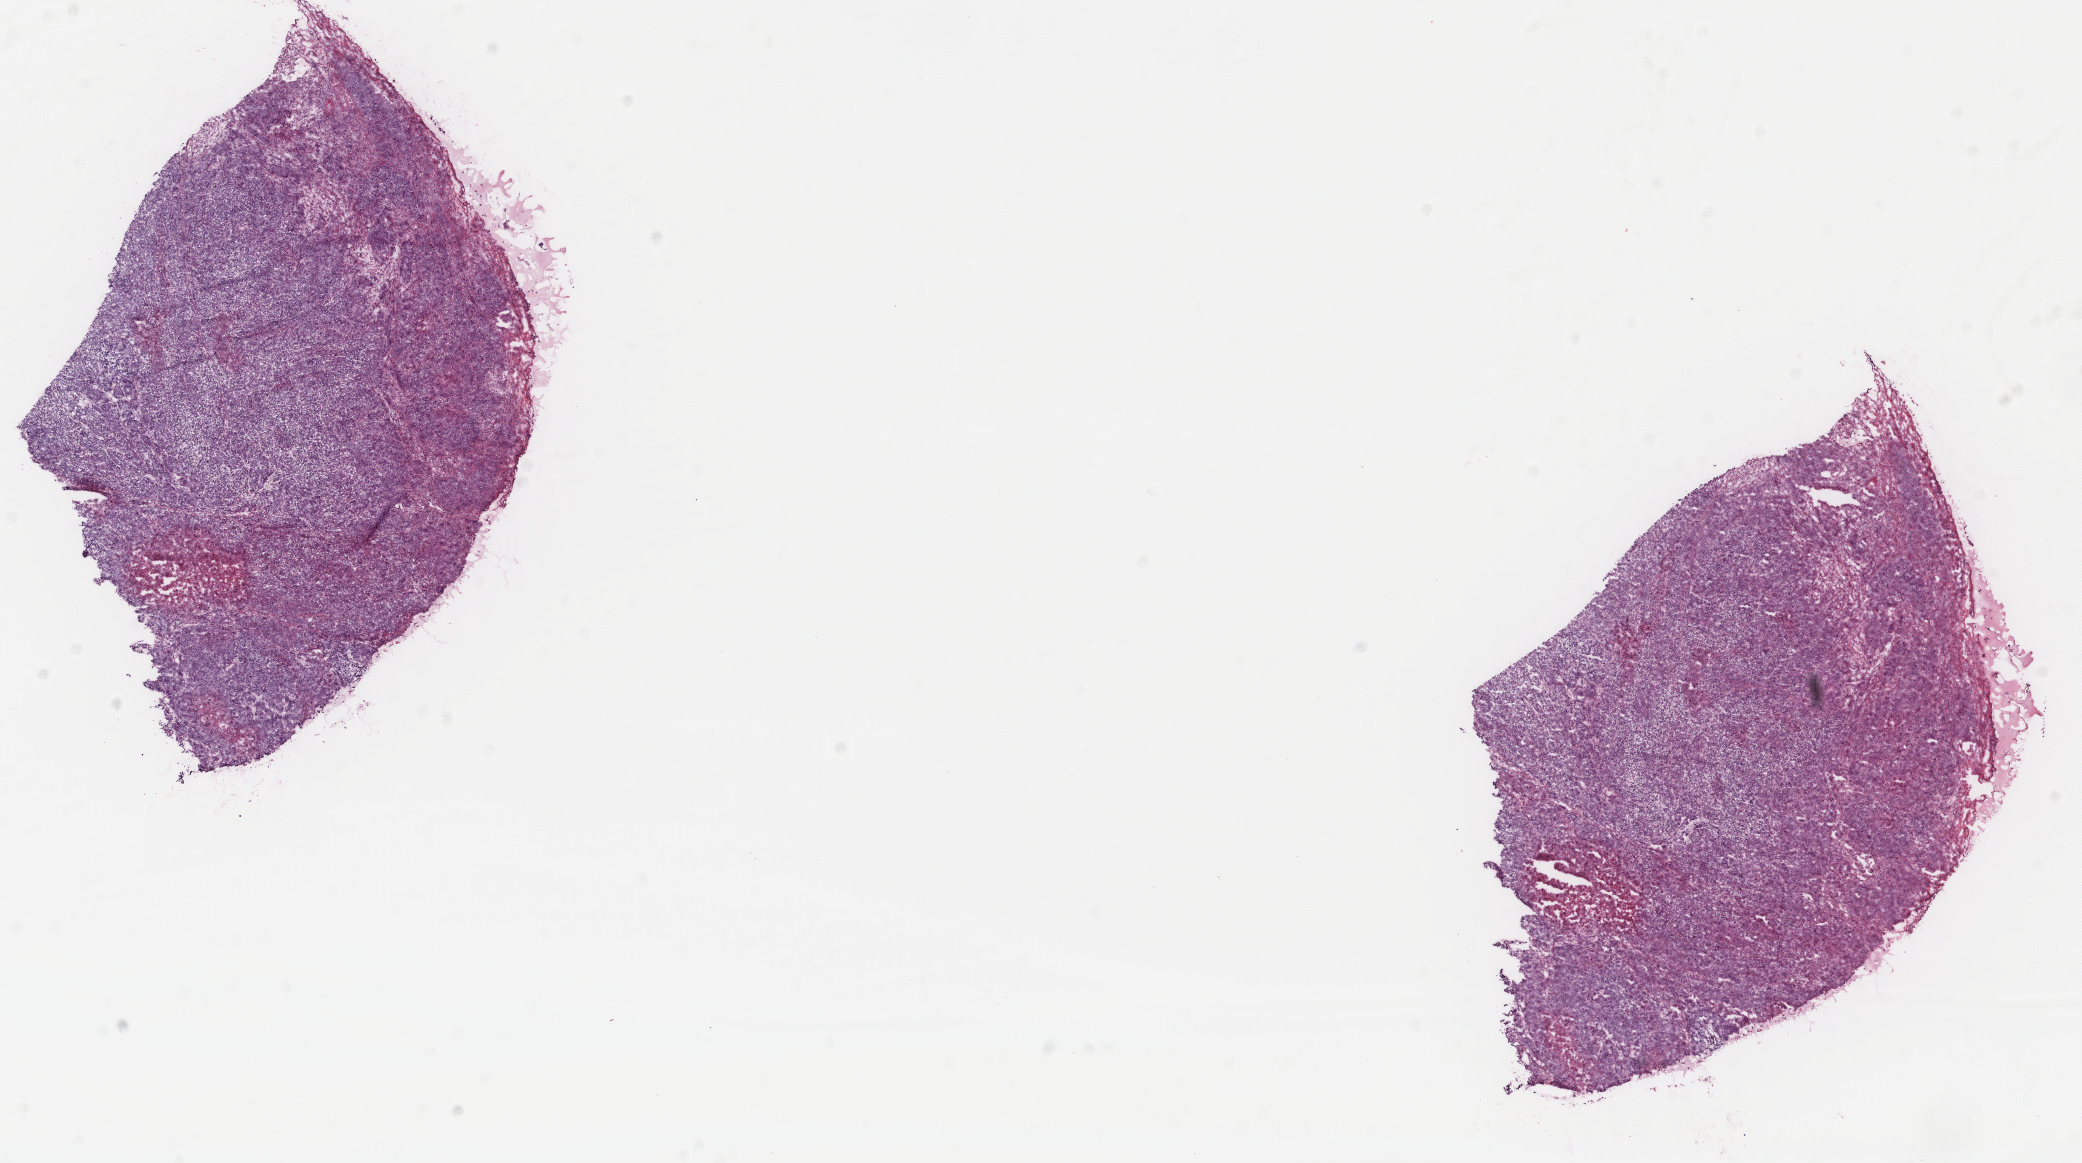
Whole-slide histology image, H&E — shown as a low-resolution overview of the whole scanned area (about 16.5 x 9.2 mm, acquisition: 40x scan); frozen section from the top of the tissue portion; cervix, primary tumour sample. Patient: female, age at initial diagnosis 48 years. Histologic grade: G3 (poorly differentiated). Pathologist review of this section (percent, as recorded): tumour cells 78%, tumour nuclei 65%, normal cells 2%, stromal cells 5%, necrosis 15%. Inflammatory infiltration, as recorded: lymphocyte infiltration 5%, monocyte infiltration 0%, neutrophil infiltration 25%.
* pathologic diagnosis: Squamous cell carcinoma, large cell, nonkeratinizing, NOS (cervix uteri)
* FIGO stage: IB2